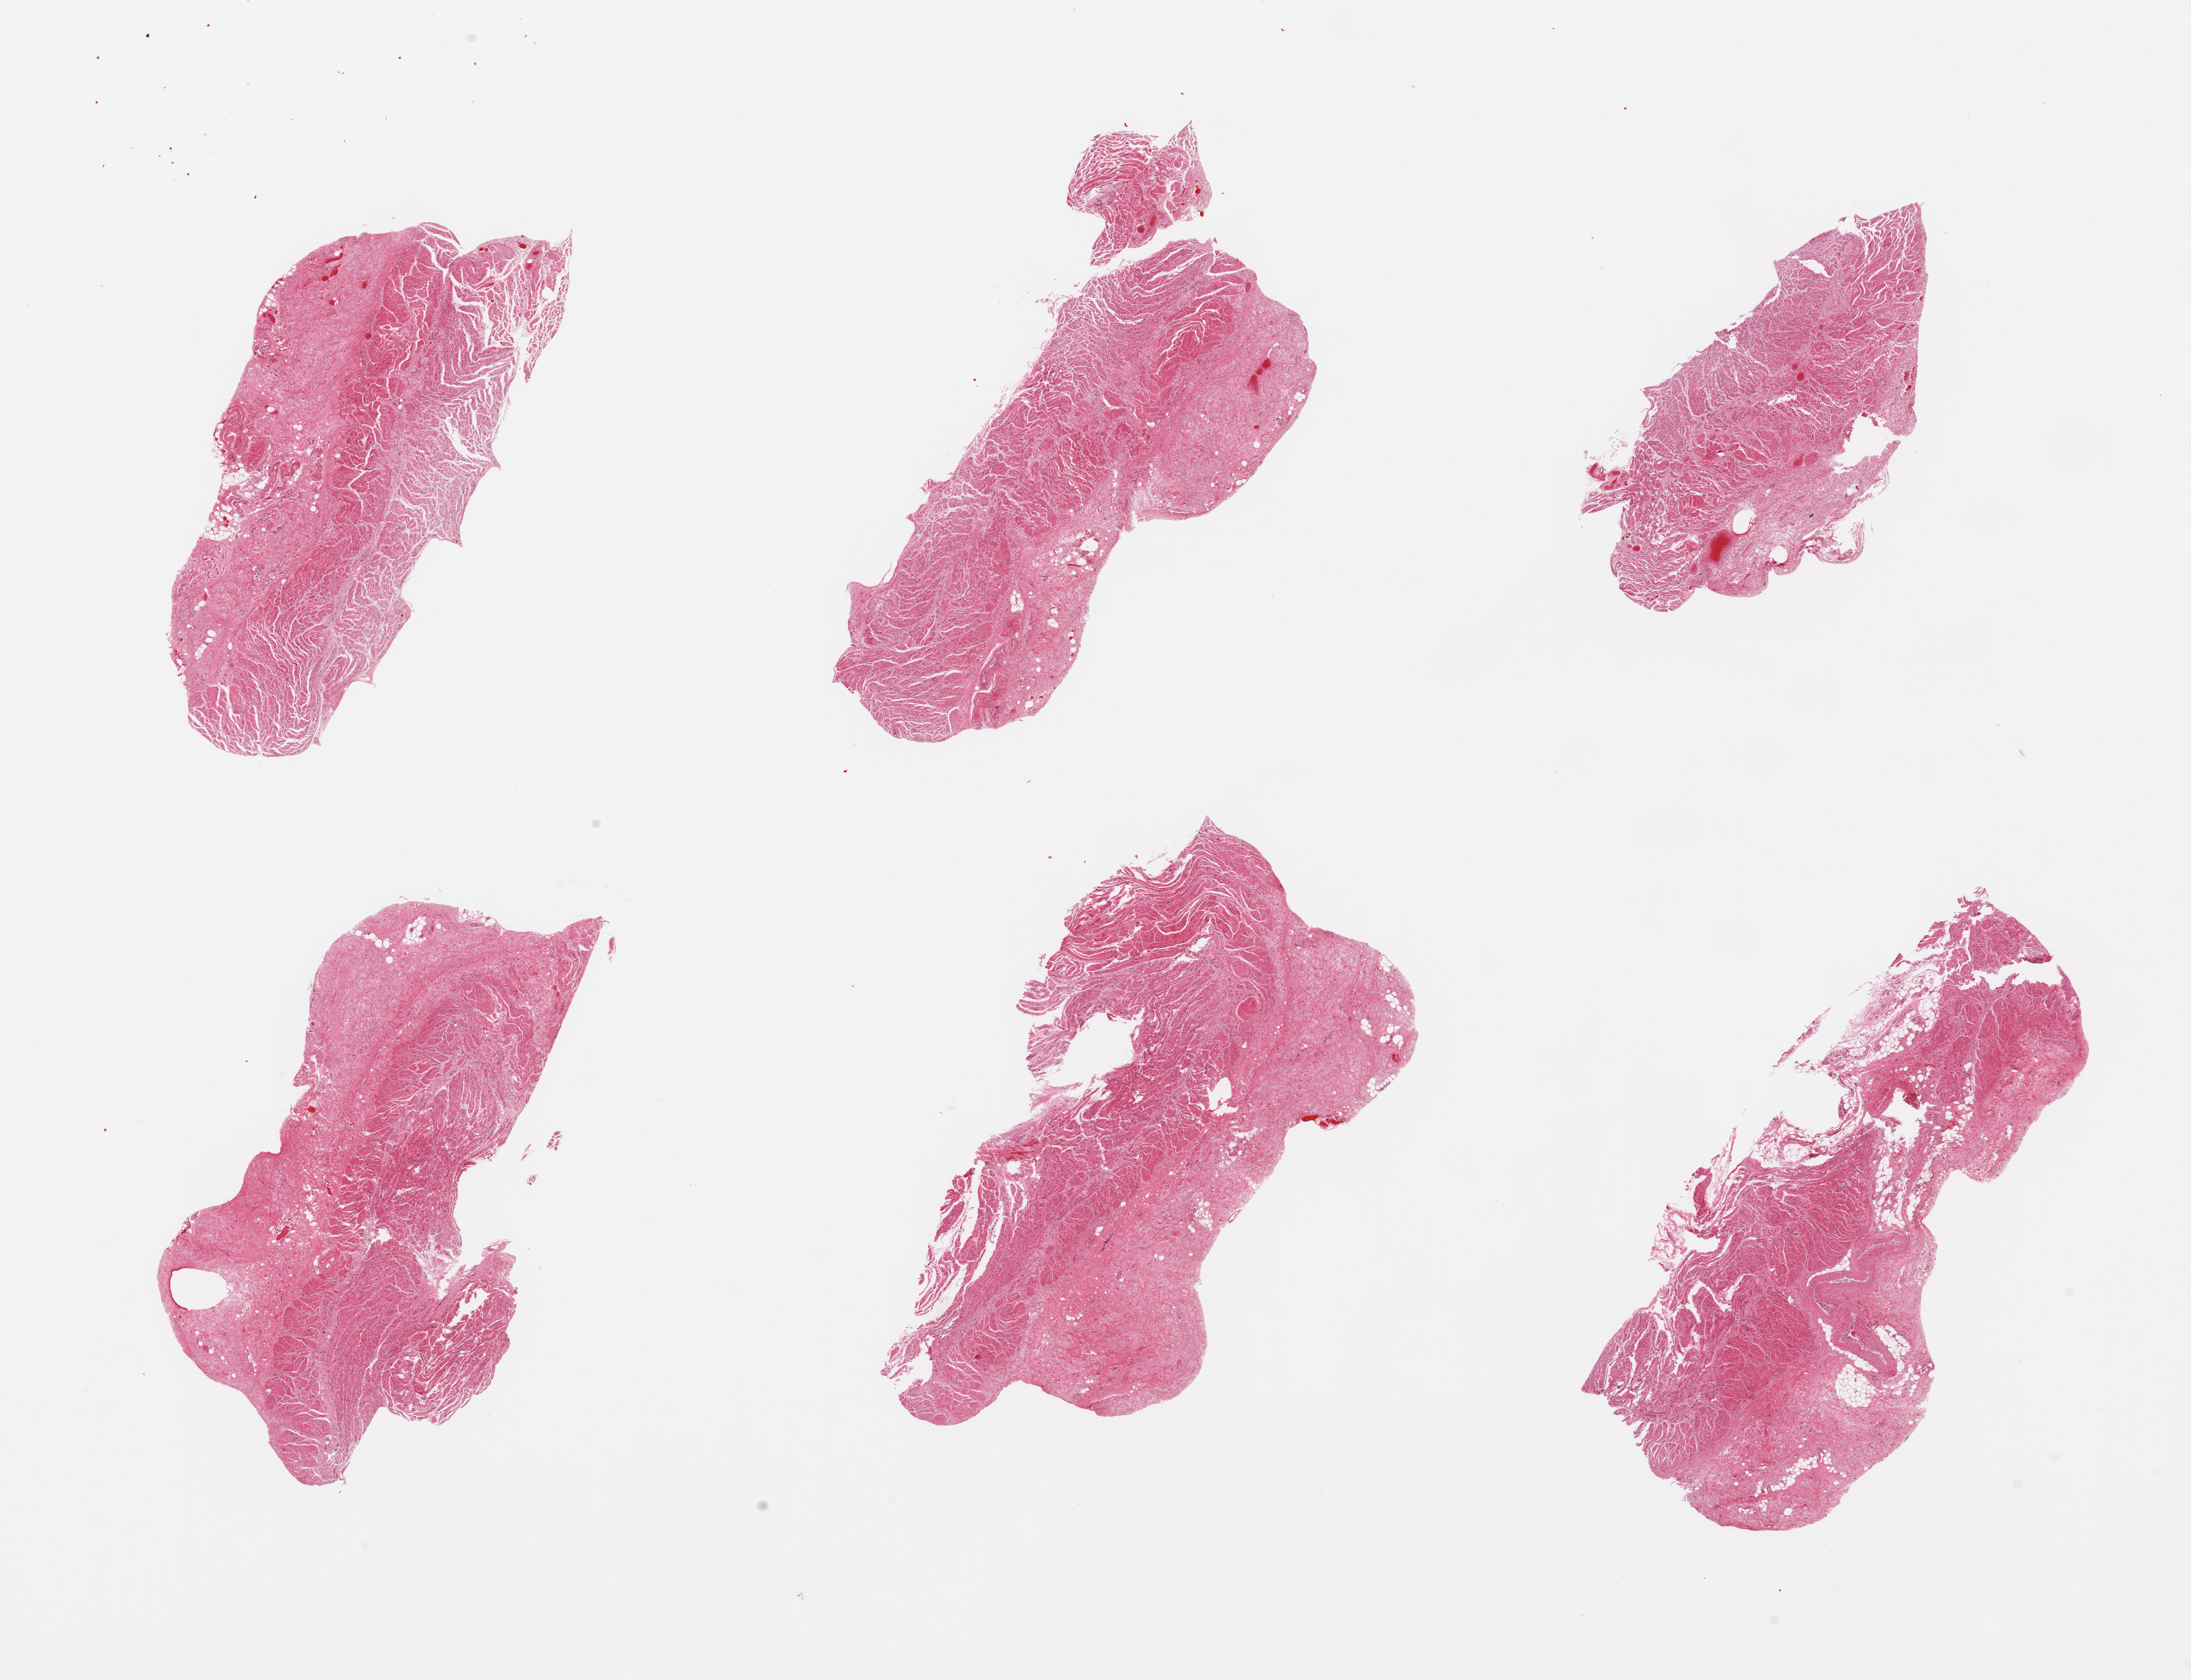
Digitized hematoxylin and eosin (H&E)-stained section — whole scanned area (about 23.6 x 18.1 mm) shown as a low-resolution overview, PAXgene-fixed, paraffin-embedded tissue, target tissue: gastroesophageal junction, tissue donor sample. Donor: male.
Reviewer comment on this tissue sample: 6 pieces, confirmed target muscularis.